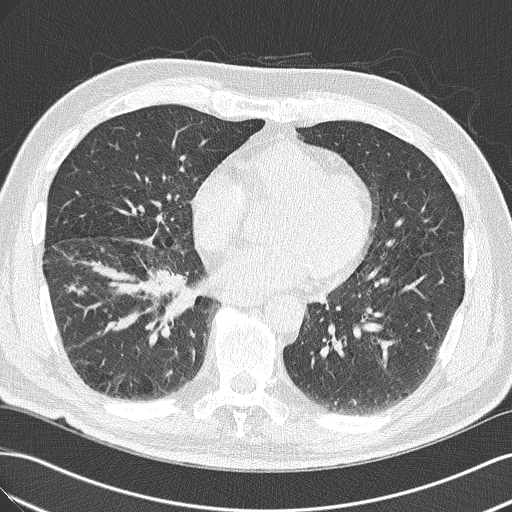
Chest CT (low-dose screening protocol), one axial image. Baseline annual screen. Lung window (W 1500 / L -600 HU). Lung (sharp) reconstruction kernel (B50f). 120 kVp. Slice 95 of 143 in the series. 512 × 512 image matrix, field of view 360 × 360 mm. Male, age 65 years at enrolment. Current smoker at enrolment.
Expert reader's lesion annotation, bounding box (x1, y1, x2, y2) in pixels: (104, 244, 203, 338). Reader record for this screening exam (exam-level; its link to the box is not recorded): non-calcified nodule or mass ≥4 mm, right upper lobe, 18 × 13 mm, spiculated (stellate) margins, soft tissue attenuation. Later outcome: lung cancer diagnosed 14 days after this screen — adenocarcinoma, NOS, right lower lobe, poorly differentiated (G3), stage IIIA (AJCC 6th edition), 40 mm at pathology.